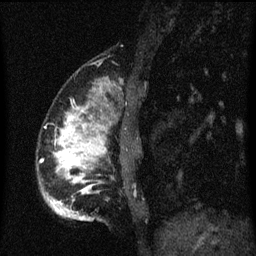
Breast MRI (dynamic contrast-enhanced), one sagittal slice; position 16 of 60 along the scan axis; dynamic contrast-enhanced series, image 2 of 3 at this slice position (ordered by acquisition); 1.5 T; TE 4.2 ms, TR 8.4 ms; 2 mm slice thickness; 256 × 256 image matrix, field of view 180 × 180 mm. Female patient, age 34 years. Case-level facts recorded for this patient, not image findings: setting: breast cancer imaged before/during neoadjuvant chemotherapy; receptor status: HR-positive, HER2-negative.
Annotated regions visible in this slice (semi-automatically segmented with operator editing):
- analysis volume of interest (the breast-tissue region the enhancement analysis was run in; not a lesion): bounding box <38,68,141,221> (left, top, right, bottom; pixels)
- tumour enhancement mask (voxels above the 70 % enhancement threshold inside the analysis volume of interest): <56,110,107,221>